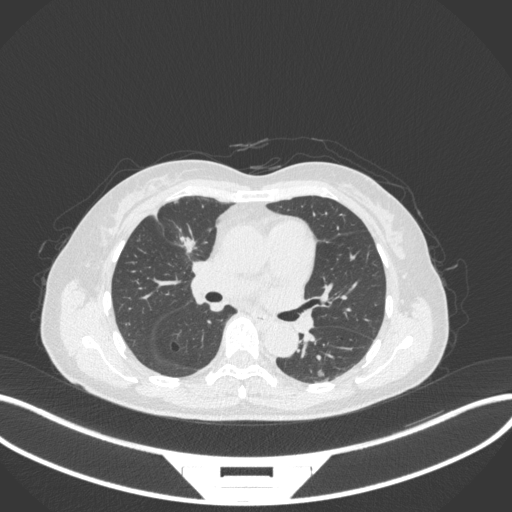
Chest CT, one axial slice; slice 167 of 282 in the series (ordered by position); reconstruction kernel B31f; lung window (W 1500 / L -600 HU); 1 mm slice thickness; 512 × 512 image matrix, field of view 400 × 400 mm. Patient: female, 51 years. Case-level facts recorded for this patient, not image findings: clinical TNM (as recorded): T1c N0 M0; histopathological grade: G2.
Annotated regions visible in this slice (bounding box drawn by a radiologist):
- lung tumour (recorded histology: adenocarcinoma): bounding box (x1, y1, x2, y2) in pixels: (175, 231, 199, 255)